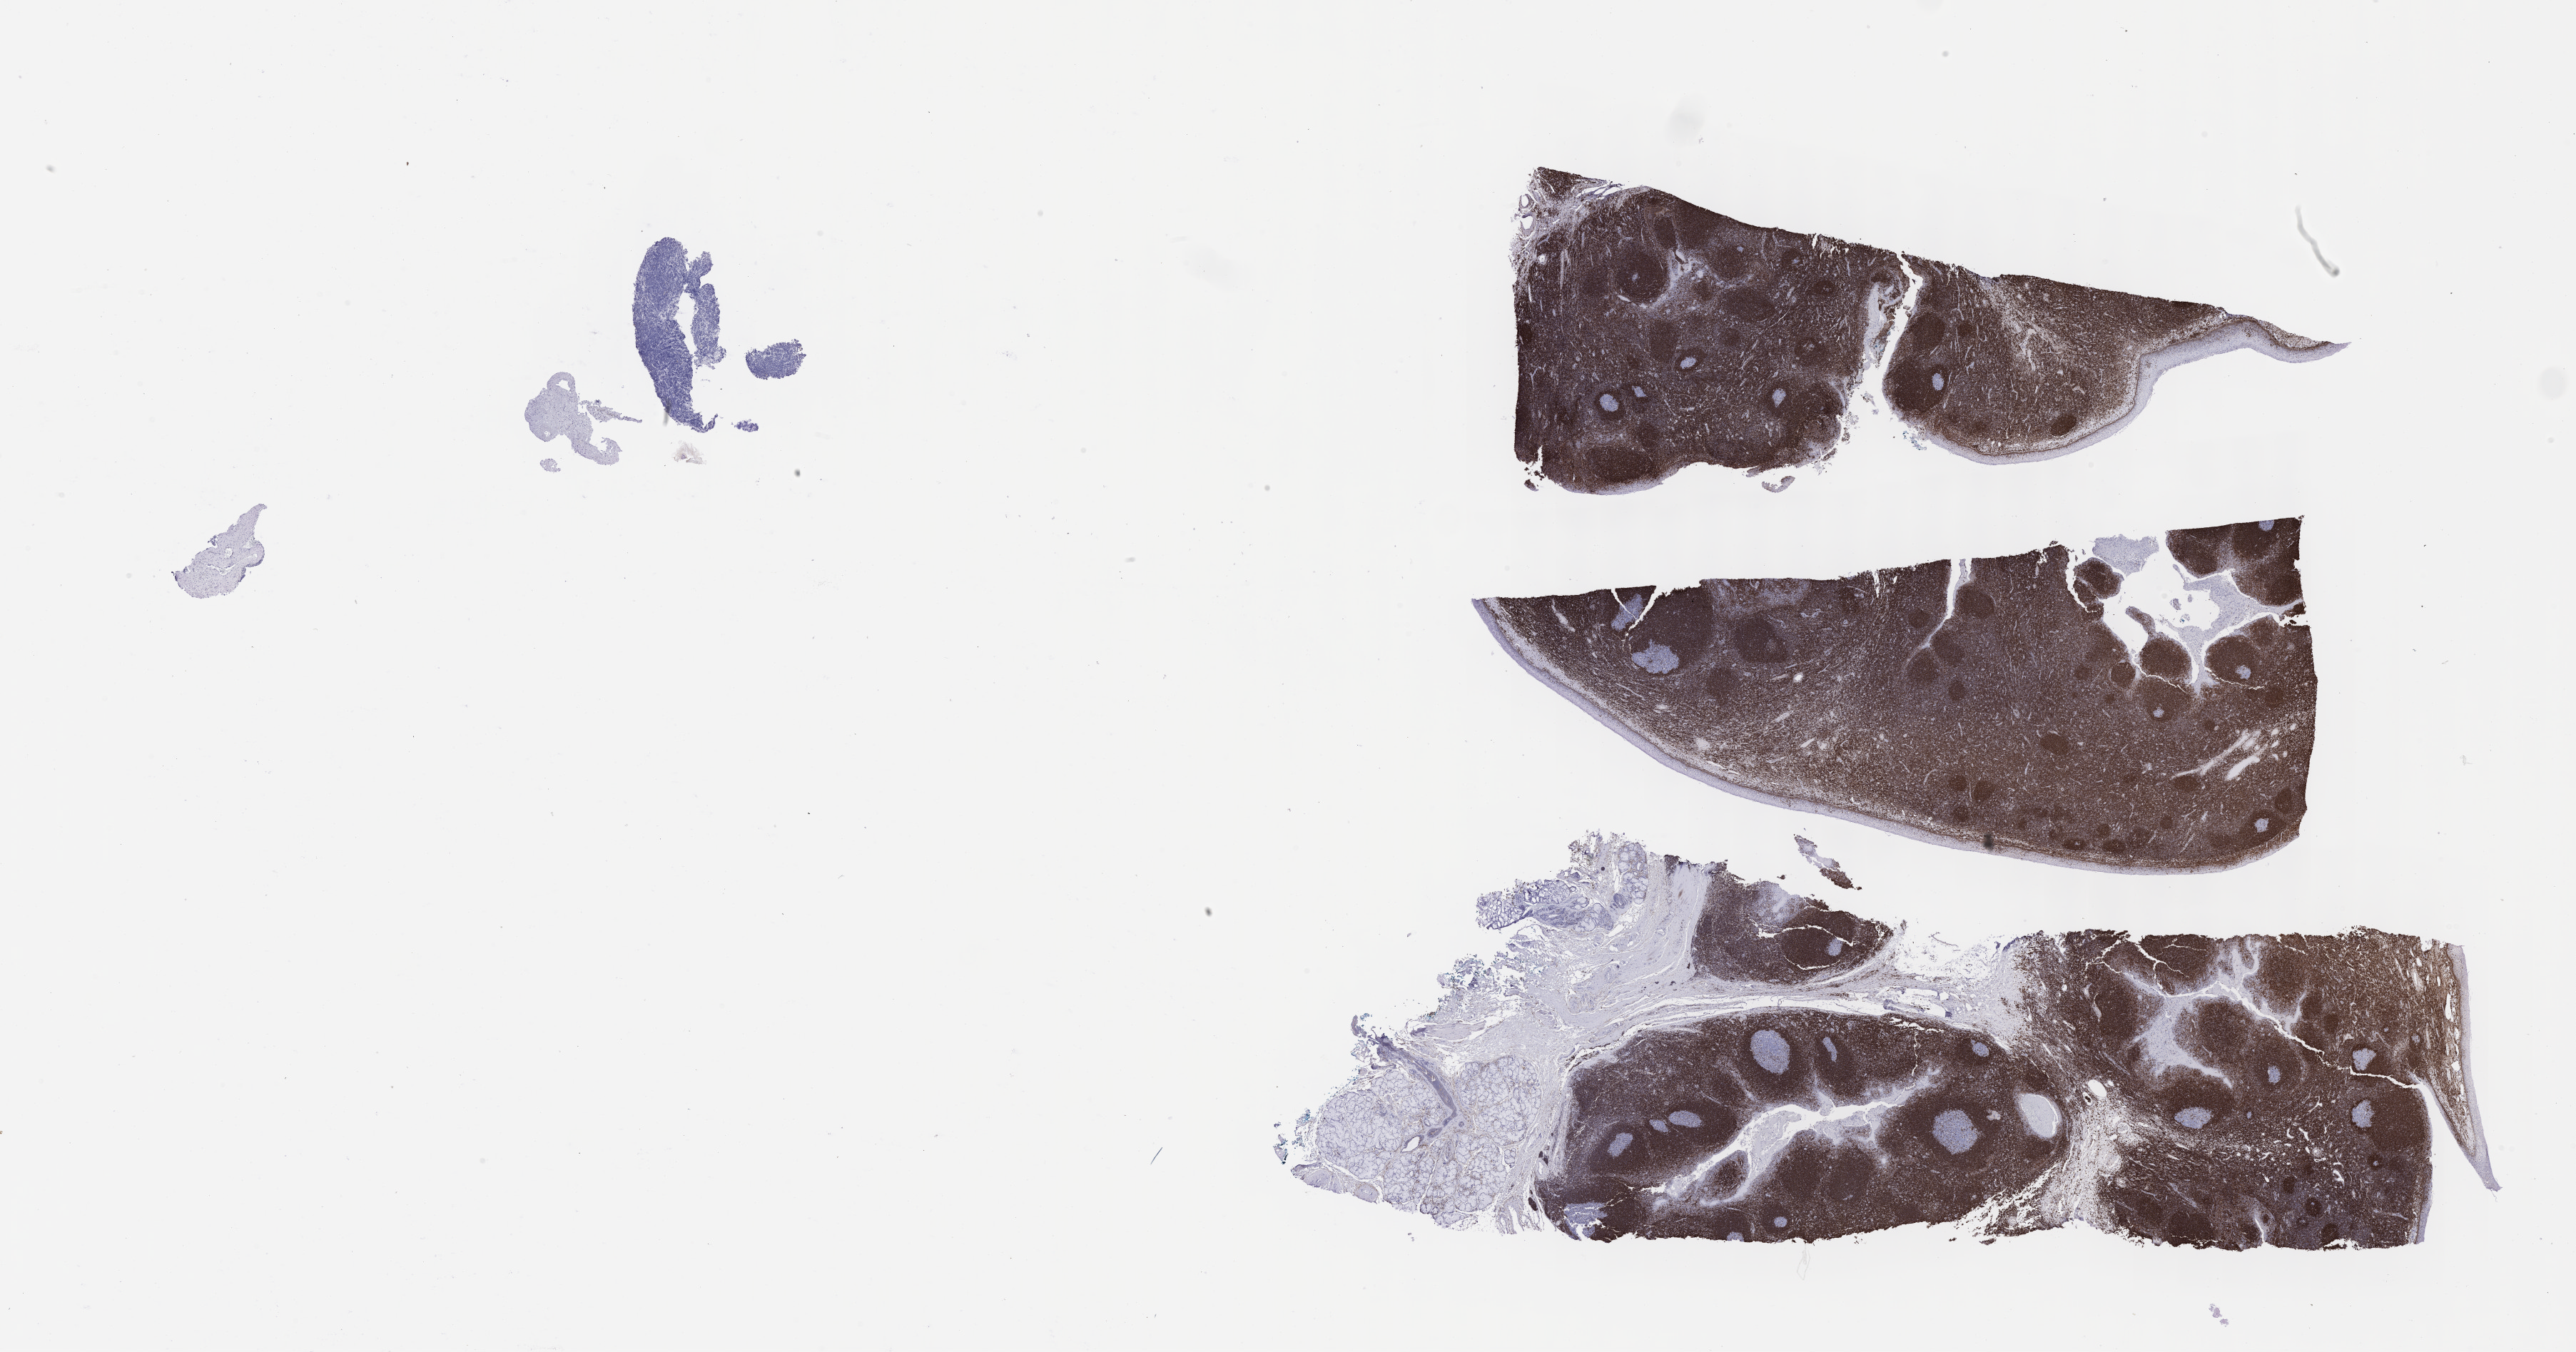
Whole-slide image, immunohistochemical stain for BCL2, whole scanned area (about 29.2 x 15.3 mm) shown as a low-resolution overview. Specimen: tumor tissue. Site: abdomen proper. Patient: female, age at initial diagnosis 7 years.
Diagnosis: Burkitt lymphoma, NOS.